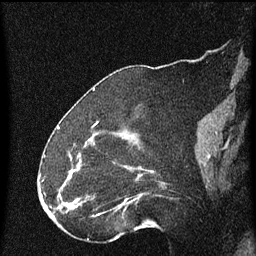
Breast MRI (dynamic contrast-enhanced), one sagittal slice; position 24 of 60 along the scan axis; dynamic contrast-enhanced series, image 2 of 4 at this slice position (ordered by acquisition); 1.5 T; TE 4.2 ms, TR 8 ms; 2 mm slice thickness; 256 × 256 image matrix, field of view 180 × 180 mm. Patient: female, 52 years.
Structures marked on this image (semi-automatic segmentation, software-assisted and operator-edited):
- analysis volume of interest (the breast-tissue region the enhancement analysis was run in; not a lesion): bounding box (x1, y1, x2, y2) in pixels: (73, 152, 167, 219)
- tumour enhancement mask (voxels above the 70 % enhancement threshold inside the analysis volume of interest): (73, 170, 125, 215)